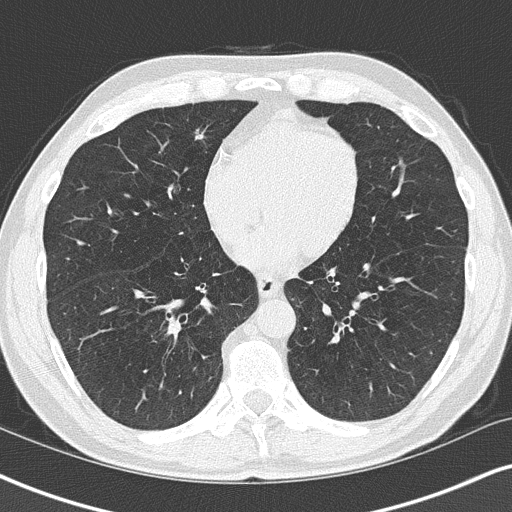
Axial slice from a low-dose chest CT screening exam. Second screening round (one year after baseline). Lung window (W 1500 / L -600 HU). Lung (sharp) reconstruction kernel (B50f). 120 kVp. Slice 104 of 148 in the series. Male, age 58 years at enrolment.
- Lesion marked by an expert reader, box from (x=169, y=118) to (x=221, y=161) px.
- Screening reader's record for this exam (one nodule recorded; not confirmed to be the boxed lesion): non-calcified nodule or mass ≥4 mm, right middle lobe, 8 × 8 mm, spiculated (stellate) margins, soft tissue attenuation, pre-existing on the prior screen: yes; interval growth: yes.
- Official screen result: positive, other.
- Later outcome: lung cancer diagnosed 21 days after this screen — adenocarcinoma, NOS, right middle lobe, moderately differentiated (G2), stage IIA (AJCC 6th edition), 10 mm at pathology.